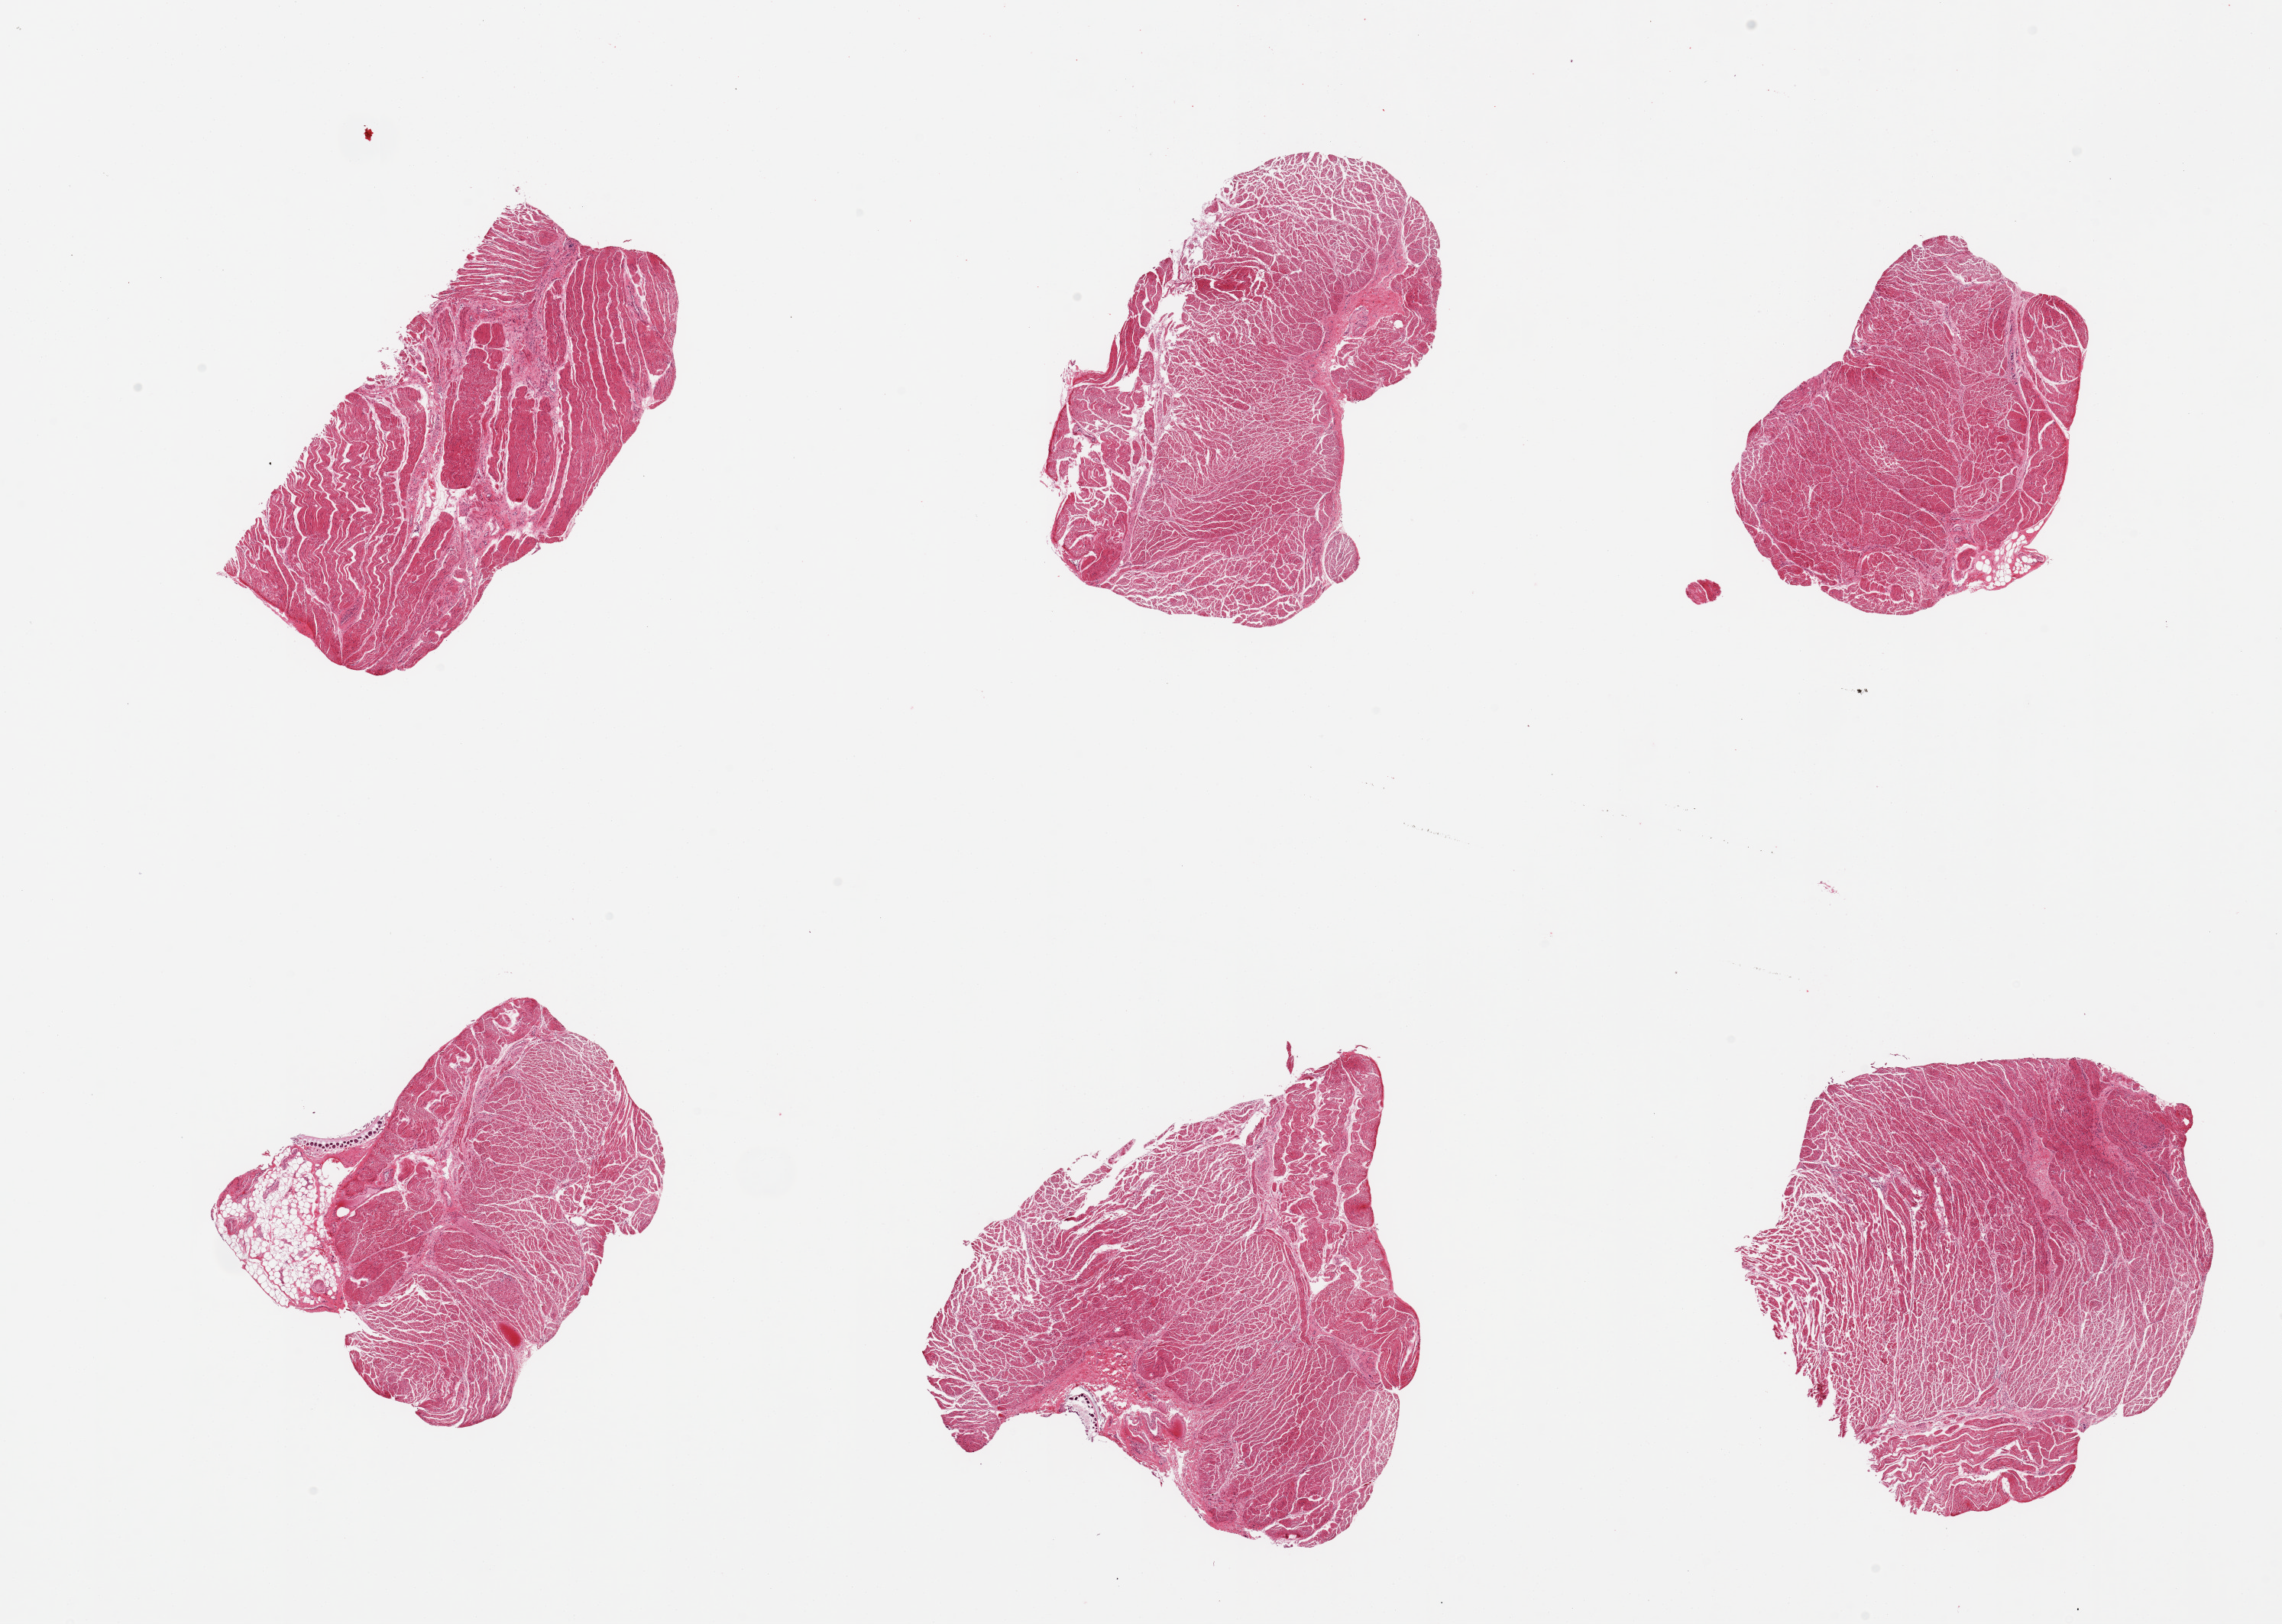
Whole-slide image, H&E stain — low-resolution overview of the scanned area, about 23.6 x 16.8 mm (from a 20x scan), PAXgene-fixed paraffin-embedded (PFPE) section, section of esophageal muscle (target tissue), tissue donor sample. Donor sex: male.
- review note (as recorded): 6 pieces; essentially well trimmed with small amounts of fat on one piece, fragments of food